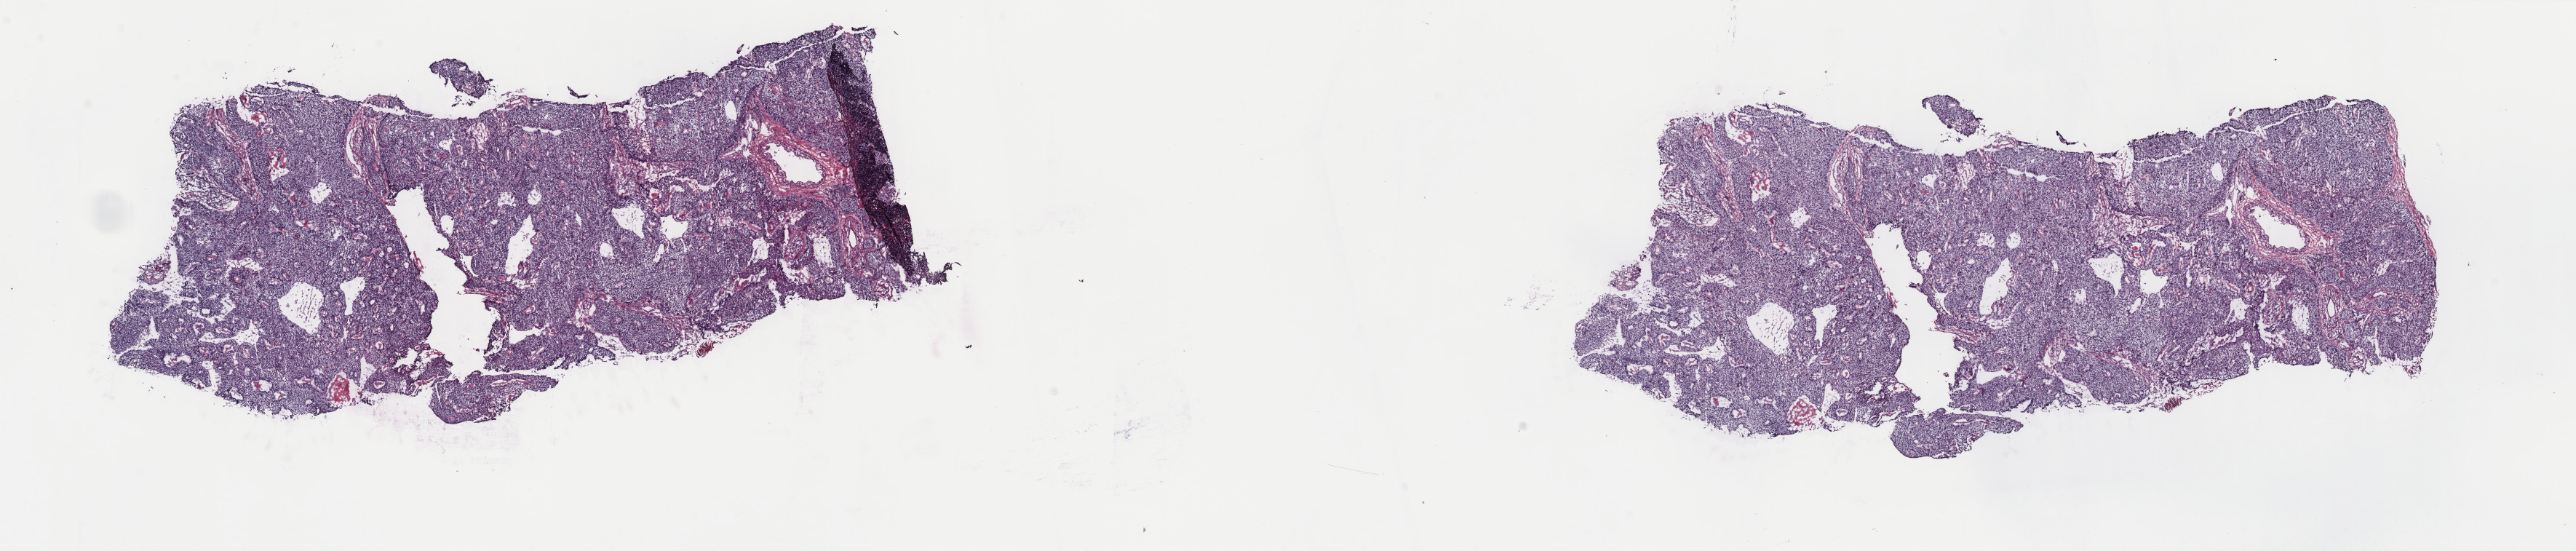
Whole-slide histology image, H&E-stained — shown as a low-resolution overview of the whole scanned area (about 28.1 x 6.0 mm, acquisition: 40x scan). Frozen section from the top of the tissue portion. Sample: primary tumour, lung. Patient: male, age at initial diagnosis 70 years. Pathologist review of this section (percent, as recorded): tumour cells 98%, tumour nuclei 95%, normal cells 0%, stromal cells 0%, necrosis 2%. Inflammatory infiltration, as recorded: lymphocyte infiltration 0%, monocyte infiltration 0%, neutrophil infiltration 0%.
TNM: T2b N0 MX. Laterality: right. AJCC pathologic stage: IIA. Pathologic diagnosis: Squamous cell carcinoma, NOS.